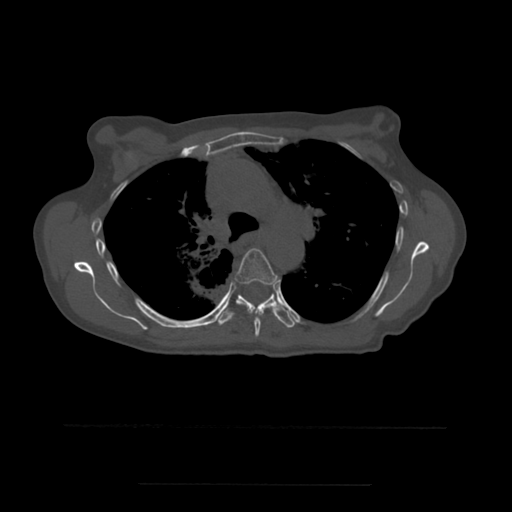
CT including the spine, one axial slice. Slice 385 of 544 in the series (ordered by position). Bone window (W 1800 / L 400 HU). 1.25 mm slice thickness. 512 × 512 image matrix, field of view 350 × 350 mm. Patient age 58 years. Case-level facts recorded for this patient, not image findings: primary cancer: lung.
Structures marked on this image (semi-automatically segmented with operator editing):
- T5 vertebra: bounding box [x1, y1, x2, y2] px = [235, 249, 278, 337]
- T6 vertebra: [216, 285, 295, 328]